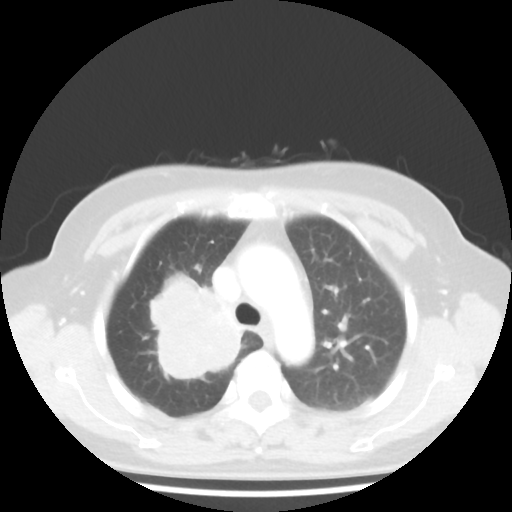
Chest CT, one axial slice. Position 32 of 44 along the scan axis. Reconstruction kernel STANDARD. Lung window (W 1500 / L -600 HU). 5 mm slice thickness. 512 × 512 image matrix, field of view 316 × 316 mm. Patient: female, 62 years. From the clinical record (not read from this slice): clinical TNM (as recorded): T3 N0 M0; histopathological grade: G3.
Structures marked on this image (rectangle marked by the reading radiologist):
- lung tumour (recorded histology: small cell carcinoma): bounding box [x1, y1, x2, y2] px = [138, 271, 253, 392]